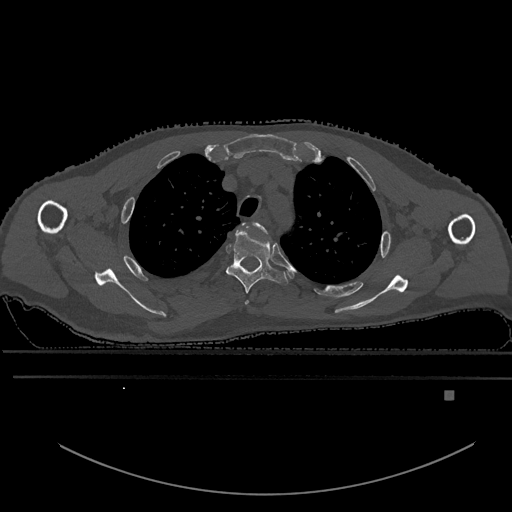
CT including the spine, one axial slice; position 454 of 969 along the scan axis; bone window (W 1800 / L 400 HU); 0.5 mm slice thickness; 512 × 512 image matrix, field of view 456 × 456 mm. Male patient, age 82 years. Case-level facts recorded for this patient, not image findings: primary cancer: prostate.
Annotated regions visible in this slice (semi-automatically segmented with operator editing):
- T2 vertebra: bounding box (x1, y1, x2, y2) in pixels: (241, 222, 267, 304)
- T3 vertebra: (226, 230, 289, 293)